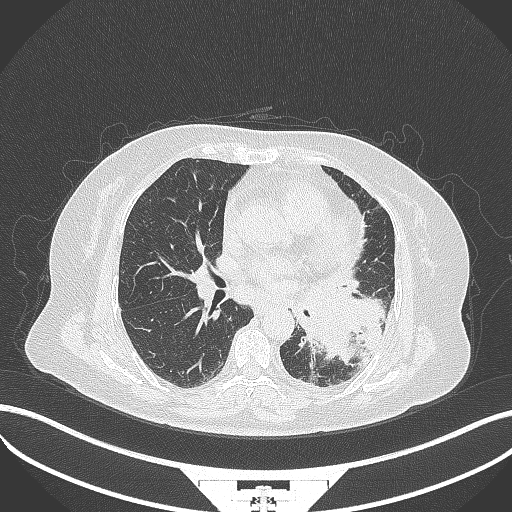
Chest CT, one axial slice; position 174 of 322 along the scan axis; reconstruction kernel B70f; lung window (W 1500 / L -600 HU); 1 mm slice thickness; 512 × 512 image matrix, field of view 400 × 400 mm. Patient: female, 69 years. Case-level facts recorded for this patient, not image findings: clinical TNM (as recorded): T2b N3 M1.
Outlined on this slice (rectangle marked by the reading radiologist):
- lung tumour (recorded histology: adenocarcinoma): bounding box <299,275,387,364> (left, top, right, bottom; pixels)